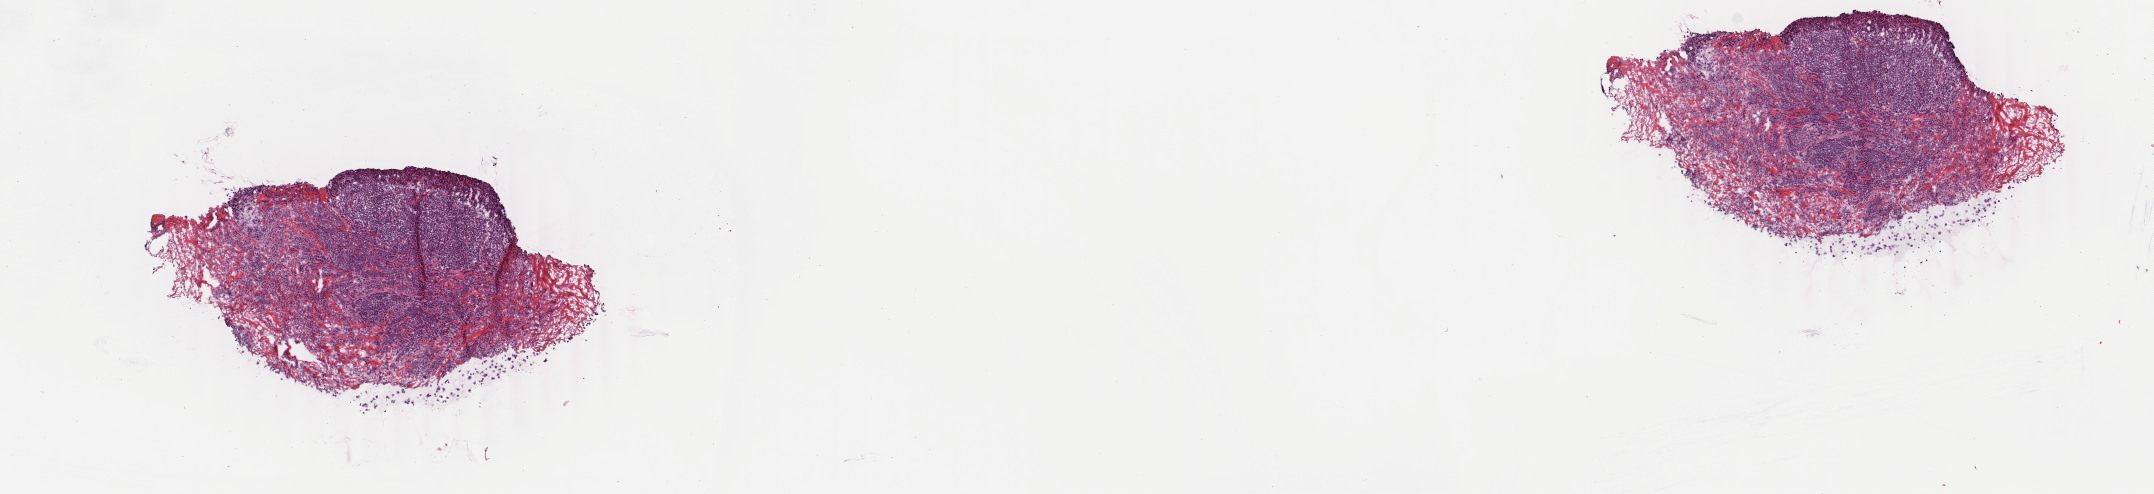
Whole-slide histology image, H&E-stained, shown as a low-resolution overview of the whole scanned area (about 17.1 x 3.9 mm), frozen section from the top of the tissue portion, metastatic tumour sample, sampled site: connective, subcutaneous and other soft tissues. Female, age 77 years at initial diagnosis. Composition of this section per pathologist review: tumour cells 100%, tumour nuclei 88%, normal cells 0%, stromal cells 0%, necrosis 0%. Inflammatory infiltration, as recorded: lymphocyte infiltration 0%, monocyte infiltration 0%, neutrophil infiltration 0%.
- this section: metastatic tumour tissue
- patient diagnosis: Malignant melanoma, NOS